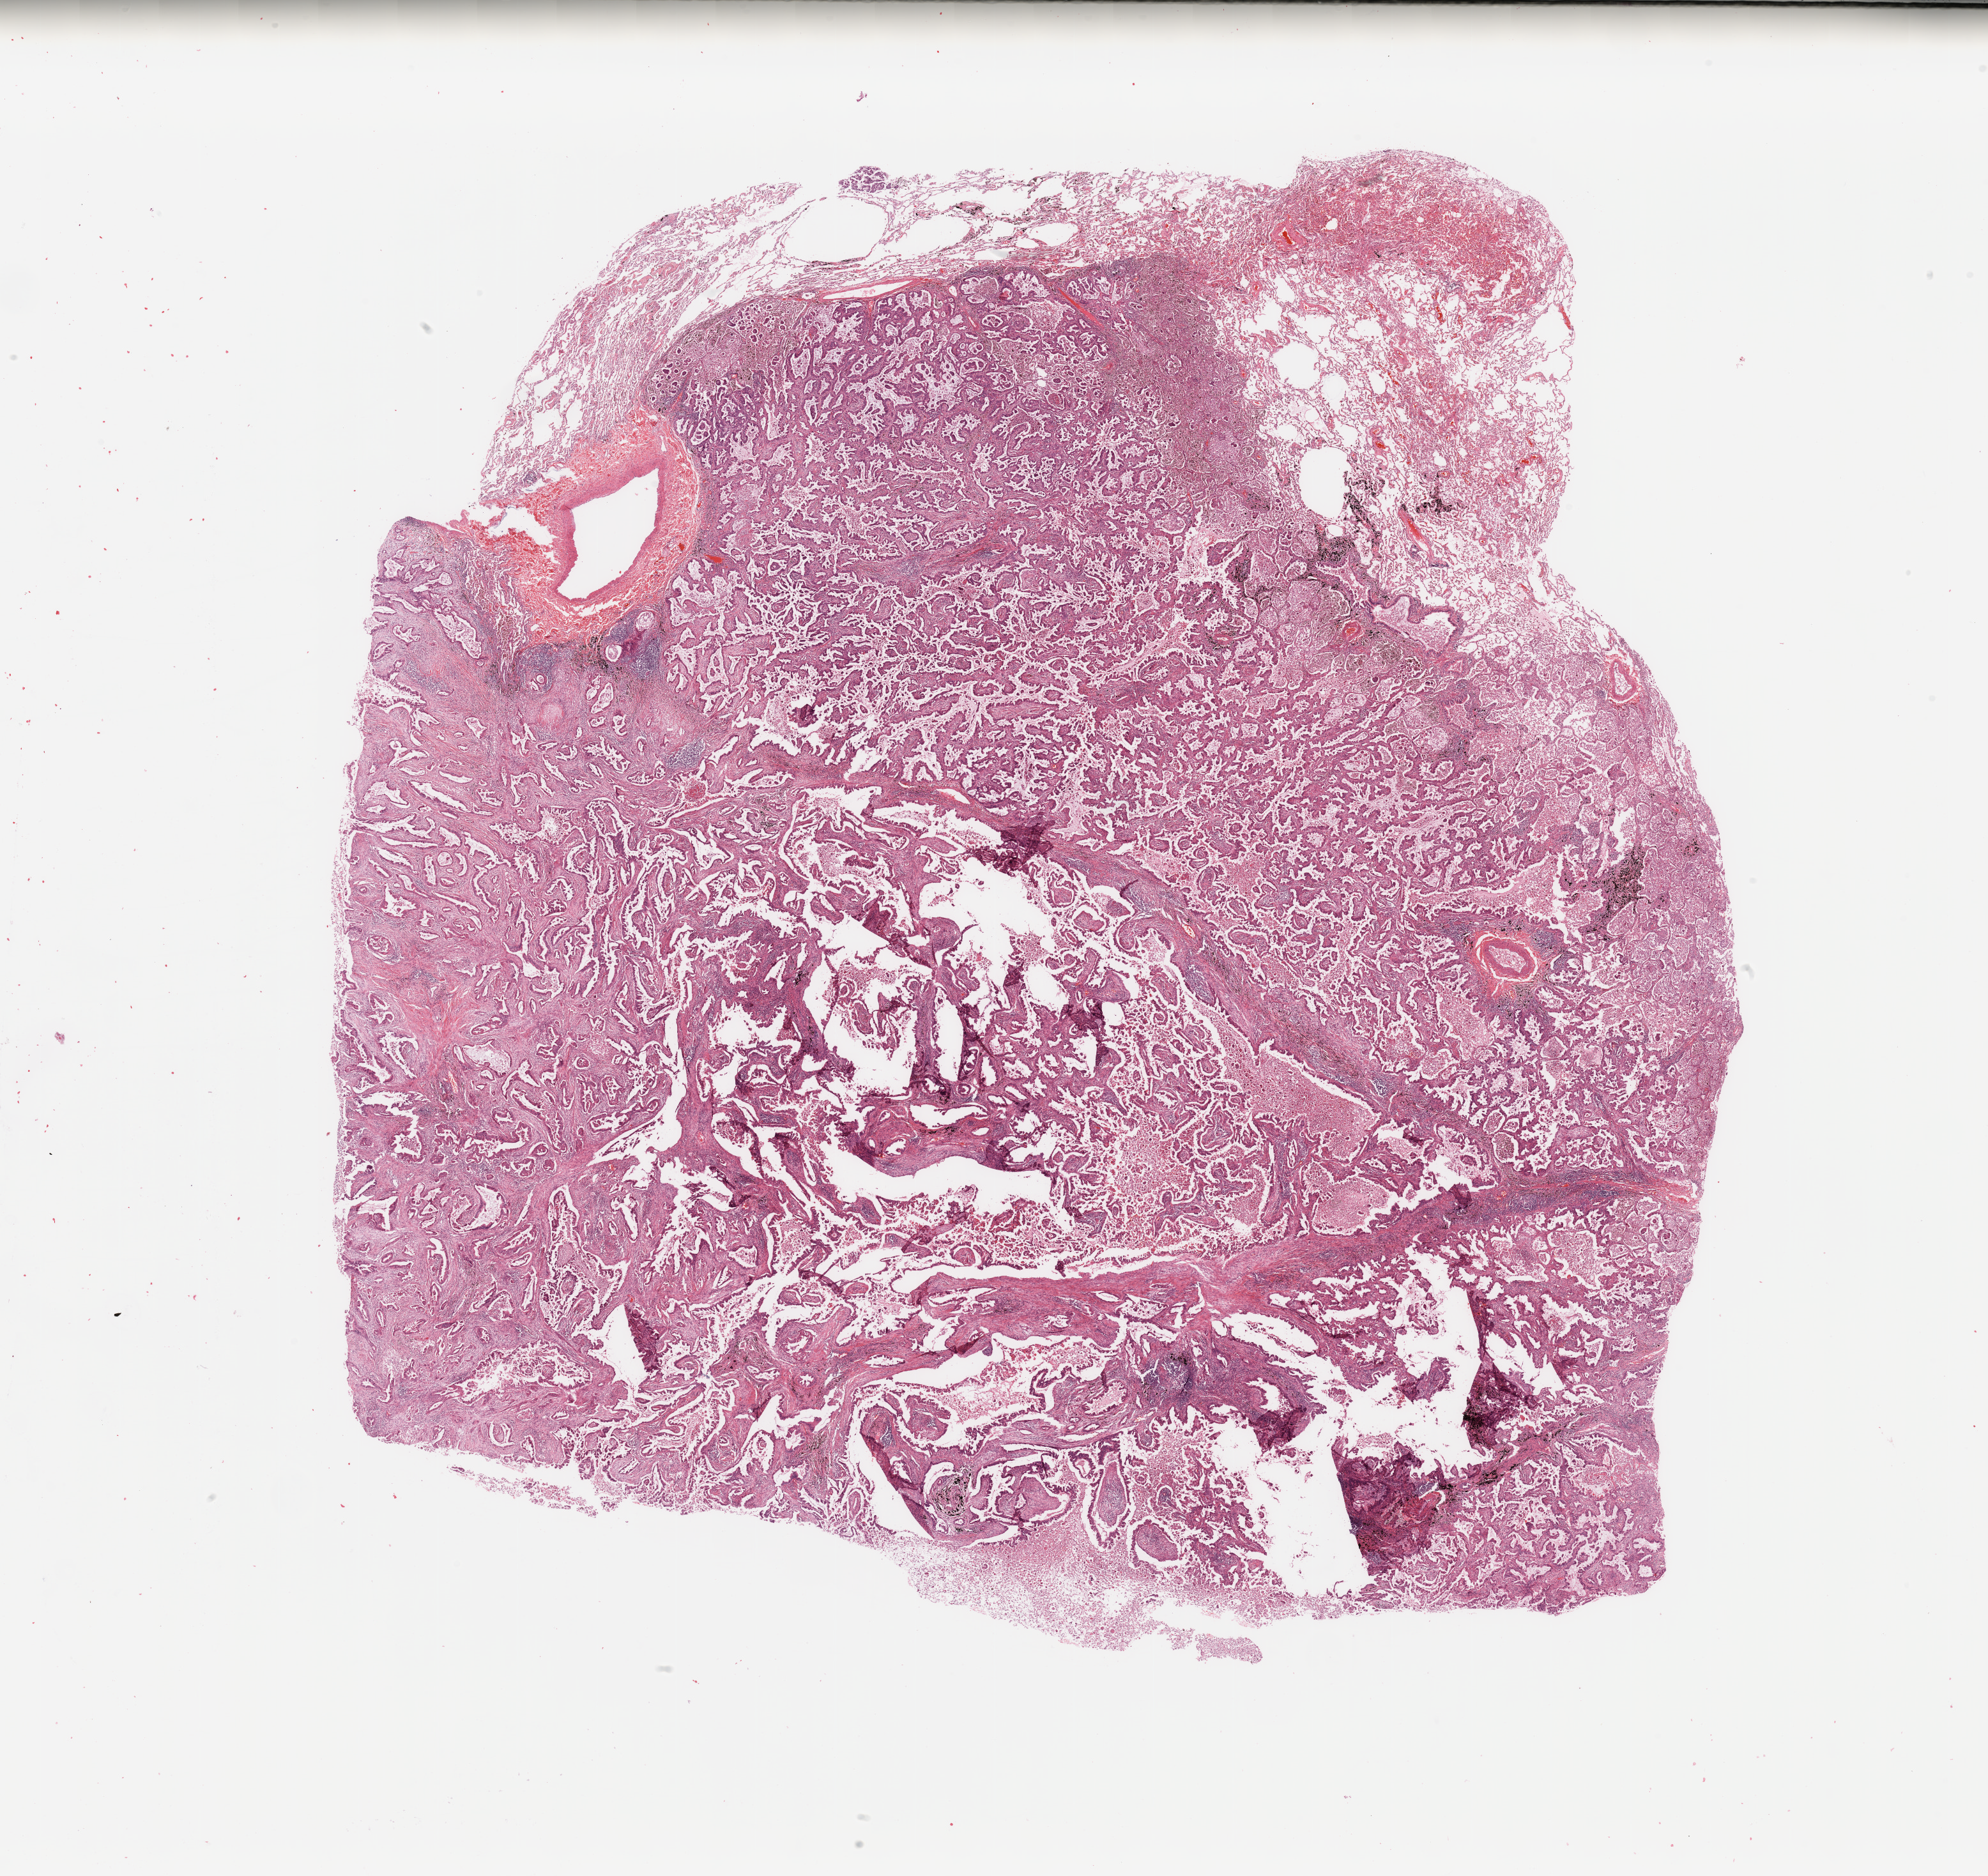
Hematoxylin and eosin (H&E) stained whole-slide image, whole scanned area (about 24.6 x 23.2 mm) shown as a low-resolution overview. Tumour tissue sample, lung. Male, 58 y/o. Histologic grade: G2 (moderately differentiated).
• diagnosis: Adenocarcinoma, NOS
• AJCC pathologic stage: IIIA